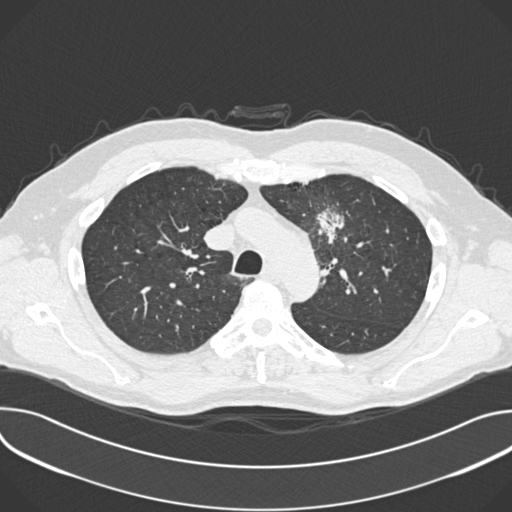
Low-dose screening chest CT, one axial slice. Position 271 of 361 along the scan axis. 120 kVp. Lung window (W 1500 / L -600 HU). 1 mm slice thickness. 512 × 512 image matrix, field of view 380 × 380 mm.
Annotated regions visible in this slice (manually delineated by an expert):
- lesion 1 (tumor, upper lobe of left lung): bounding box (x1, y1, x2, y2) in pixels: (317, 210, 344, 239)